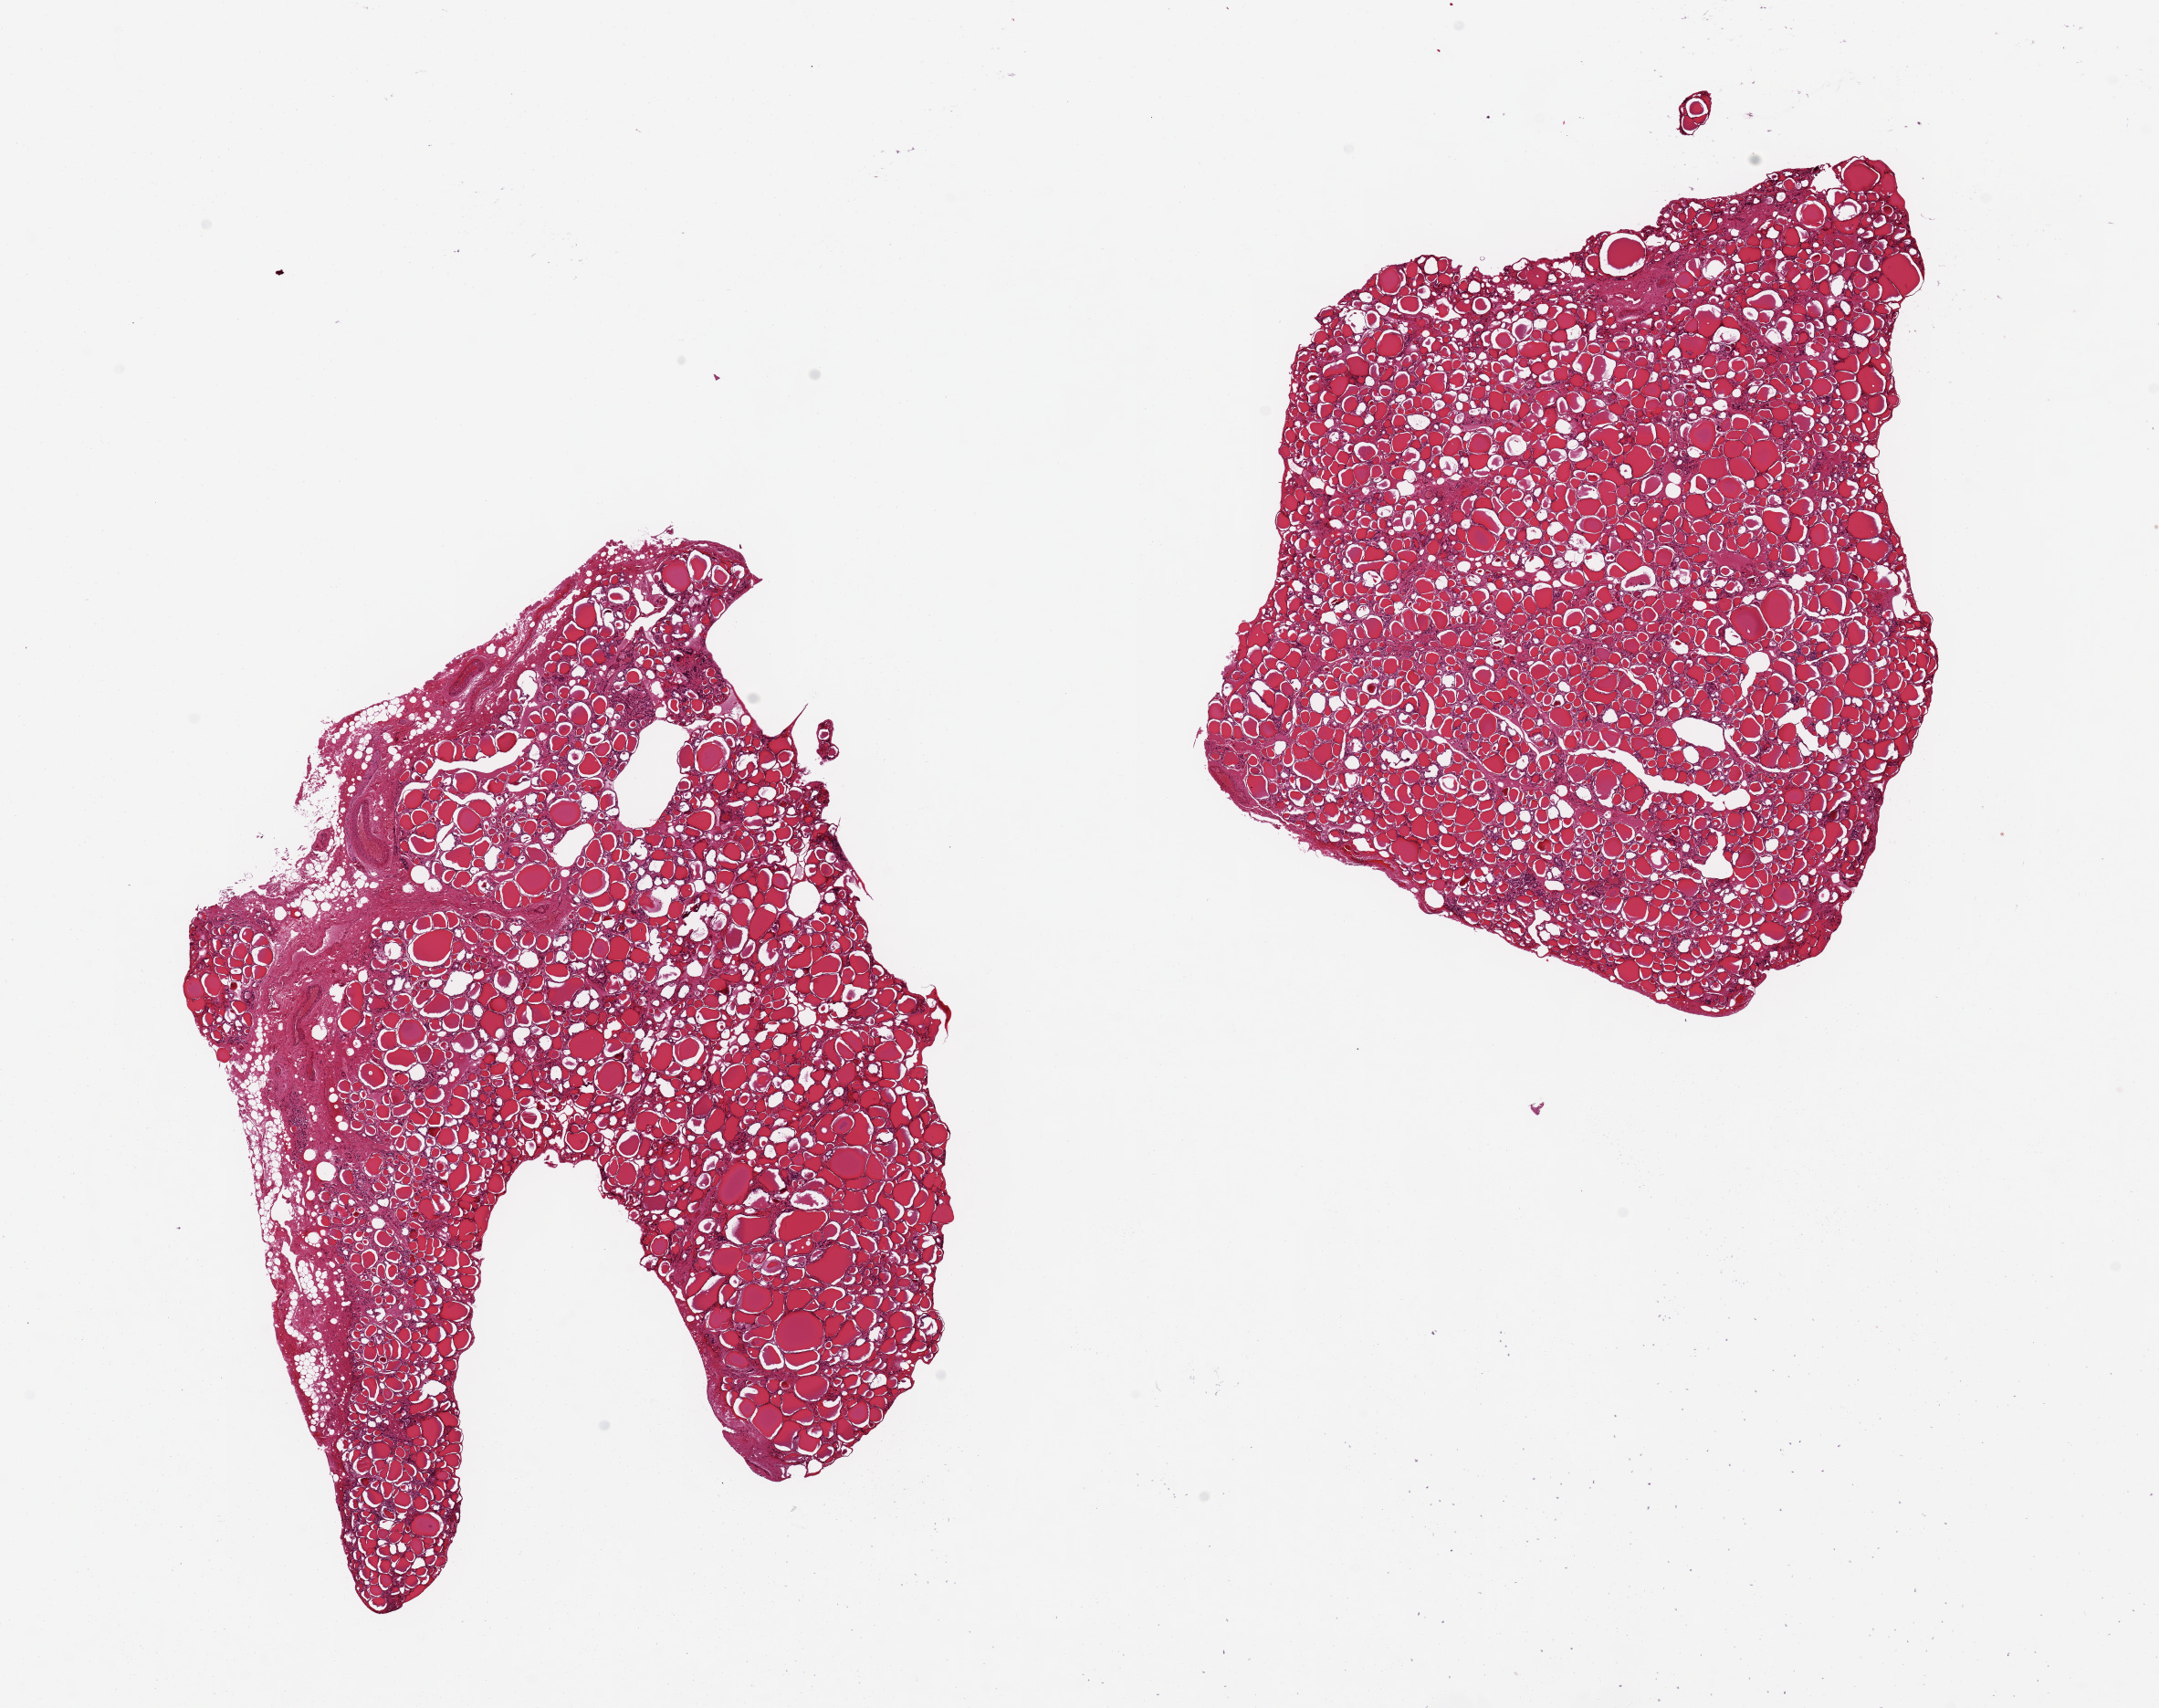
Digitized H&E-stained section, brightfield, low-resolution overview of the scanned area, about 18.7 x 14.8 mm (from a 20x scan); PAXgene-fixed paraffin-embedded (PFPE) section; target tissue: thyroid; tissue donor sample.
* review note (as recorded): 2 aliquots, ~8x5mm